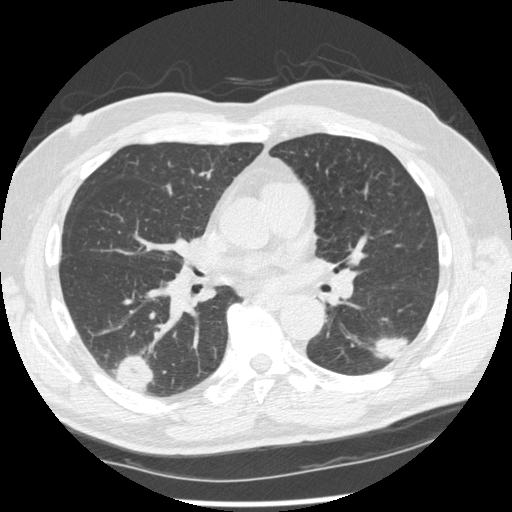
Axial slice from a low-dose chest CT screening exam; second screening round (one year after baseline); lung window (W 1500 / L -600 HU); 1.25 mm slice thickness; standard (soft-tissue) reconstruction kernel (STANDARD); 120 kVp; slice 118 of 227 in the series; 512 × 512 image matrix. Male participant, aged 74 years at enrolment.
• Expert-annotated lung lesion, bounding box [x1, y1, x2, y2] px = [368, 314, 423, 368].
• The screening reader recorded 7 non-calcified nodules or masses ≥4 mm on this exam (right upper lobe, right lower lobe, right upper lobe, right lower lobe, left lower lobe, left upper lobe, left upper lobe); which of them this box marks is not recorded.
• Official screen result: positive, other.